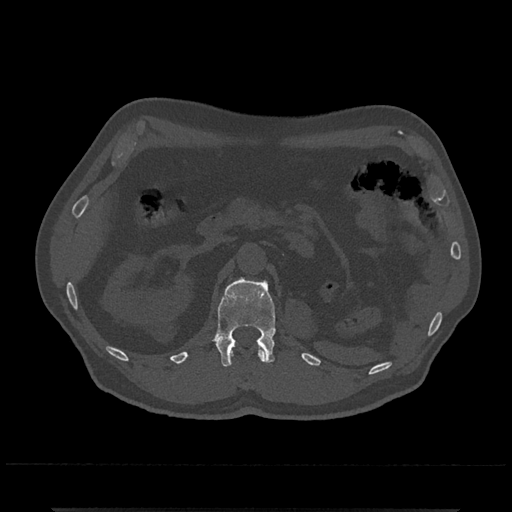
CT including the spine, one axial slice; position 377 of 797 along the scan axis; 120 kVp; bone window (W 1800 / L 400 HU); 512 × 512 image matrix. Male patient, age 67 years. Case-level facts recorded for this patient, not image findings: primary cancer: prostate.
Structures marked on this image (semi-automatically segmented with operator editing):
- L1 vertebra: bounding box [x1, y1, x2, y2] px = [212, 276, 276, 367]
- T12 vertebra: [230, 346, 267, 362]